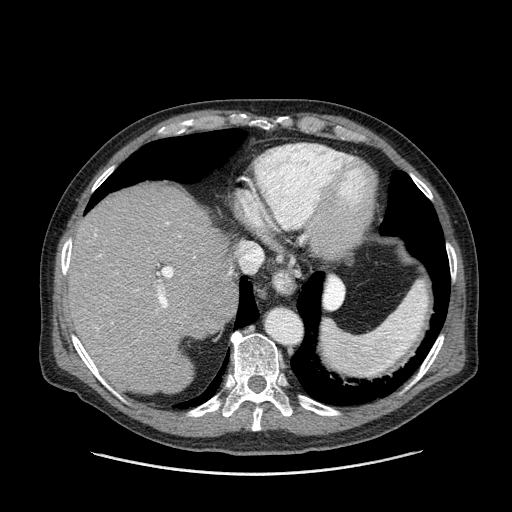
Contrast-enhanced abdominal CT (liver protocol), one axial slice. Slice 116 of 180 in the series (ordered by position). Reconstruction kernel STANDARD. One of 2 acquisitions stored at this slice position. Soft-tissue window (W 400 / L 40 HU). 2.5 mm slice thickness. 512 × 512 image matrix, field of view 420 × 420 mm. Case-level facts recorded for this patient, not image findings: diagnosis: hepatocellular carcinoma (patient treated with transarterial chemoembolisation; whether this scan precedes or follows treatment is not stated here); TNM stage (as recorded): Stage-II; Child-Pugh class: A; tumour differentiation: well differentiated; tumour nodularity: multinodular.
Outlined on this slice (semi-automatically segmented with operator editing):
- liver parenchyma outside the tumour (the mass and vessels are separate outlines, so this box may not span the whole liver): bounding box (x1, y1, x2, y2) in pixels: (68, 186, 236, 394)
- liver vessels: (94, 223, 232, 330)